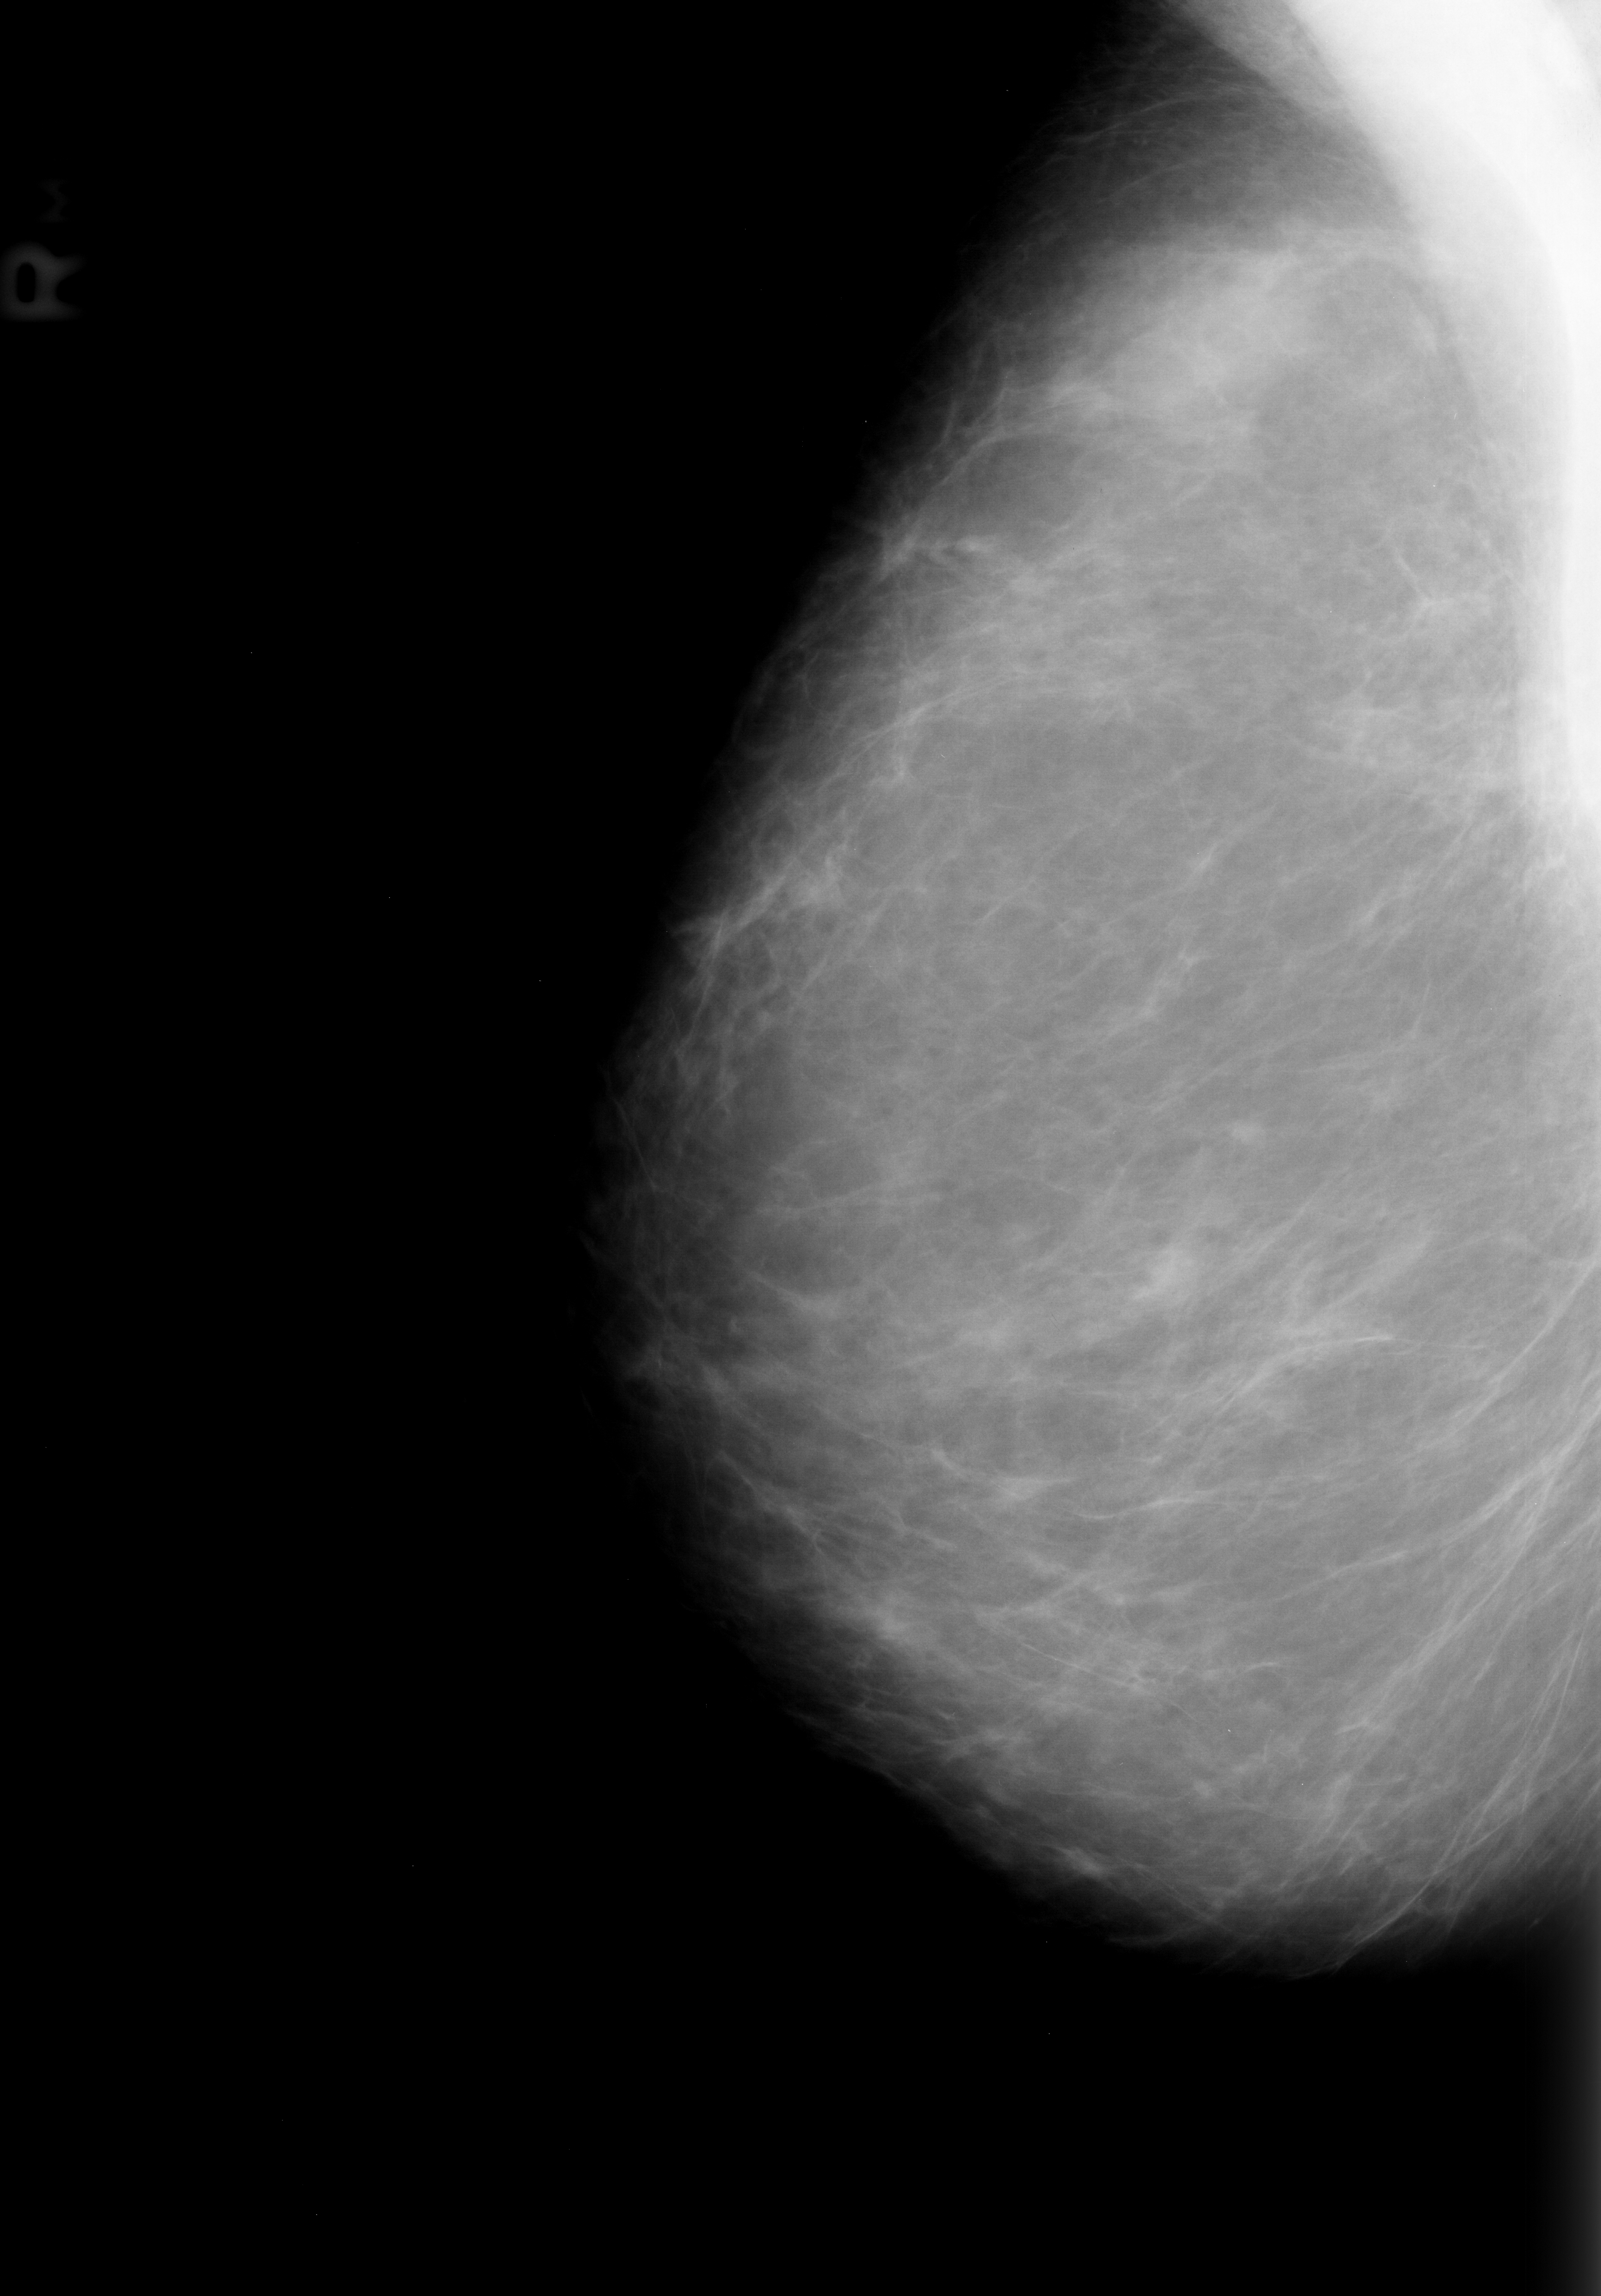
Digitized screen-film mammogram; right breast; mediolateral oblique (MLO) view; breast composition: scattered fibroglandular densities (BI-RADS density category 2 of 4); 1601 × 2296 image matrix.
Expert-marked regions of interest on this image (one box per marked abnormality):
- mass, shape asymmetric breast tissue; BI-RADS assessment category 2; outcome (as recorded, no biopsy): benign without callback (not worked up further): bounding box [x1, y1, x2, y2] px = [1066, 249, 1356, 447]